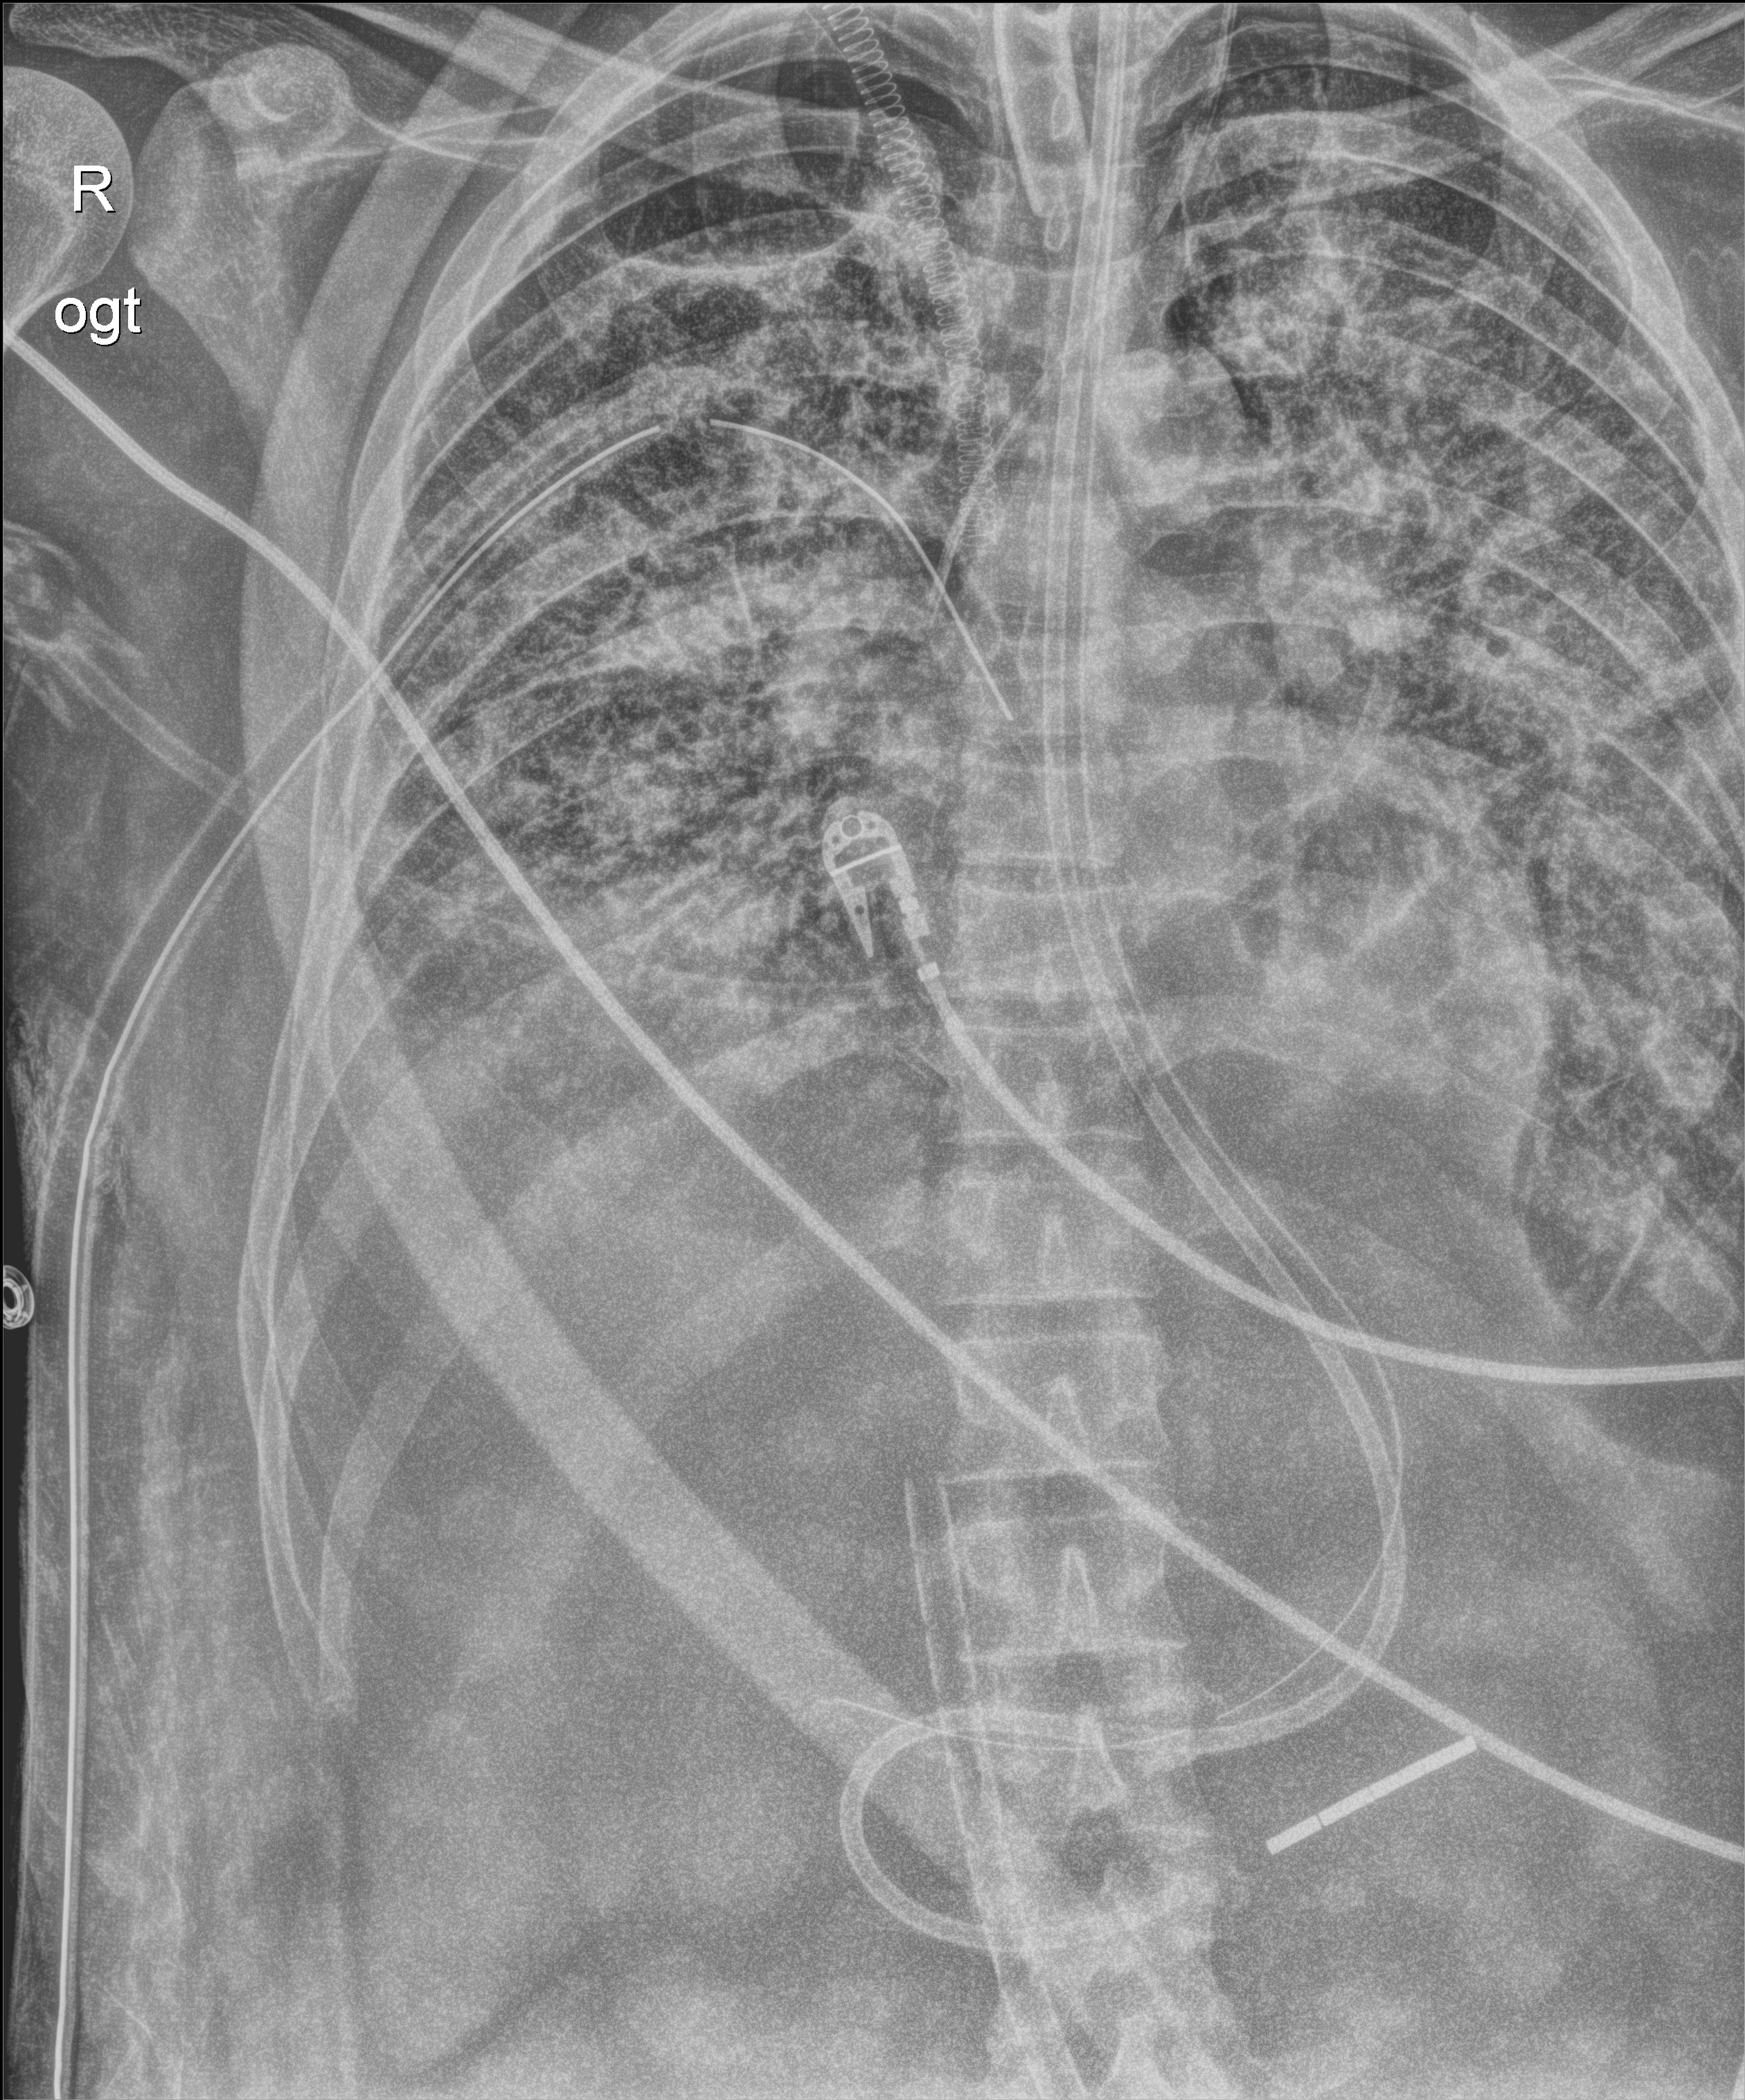
Chest radiograph. Adult patient hospitalised with COVID-19, age 18–59 years.
Admission-level facts for this patient (not findings on this image; timing relative to this image not recorded): smoking status (admission record): never.